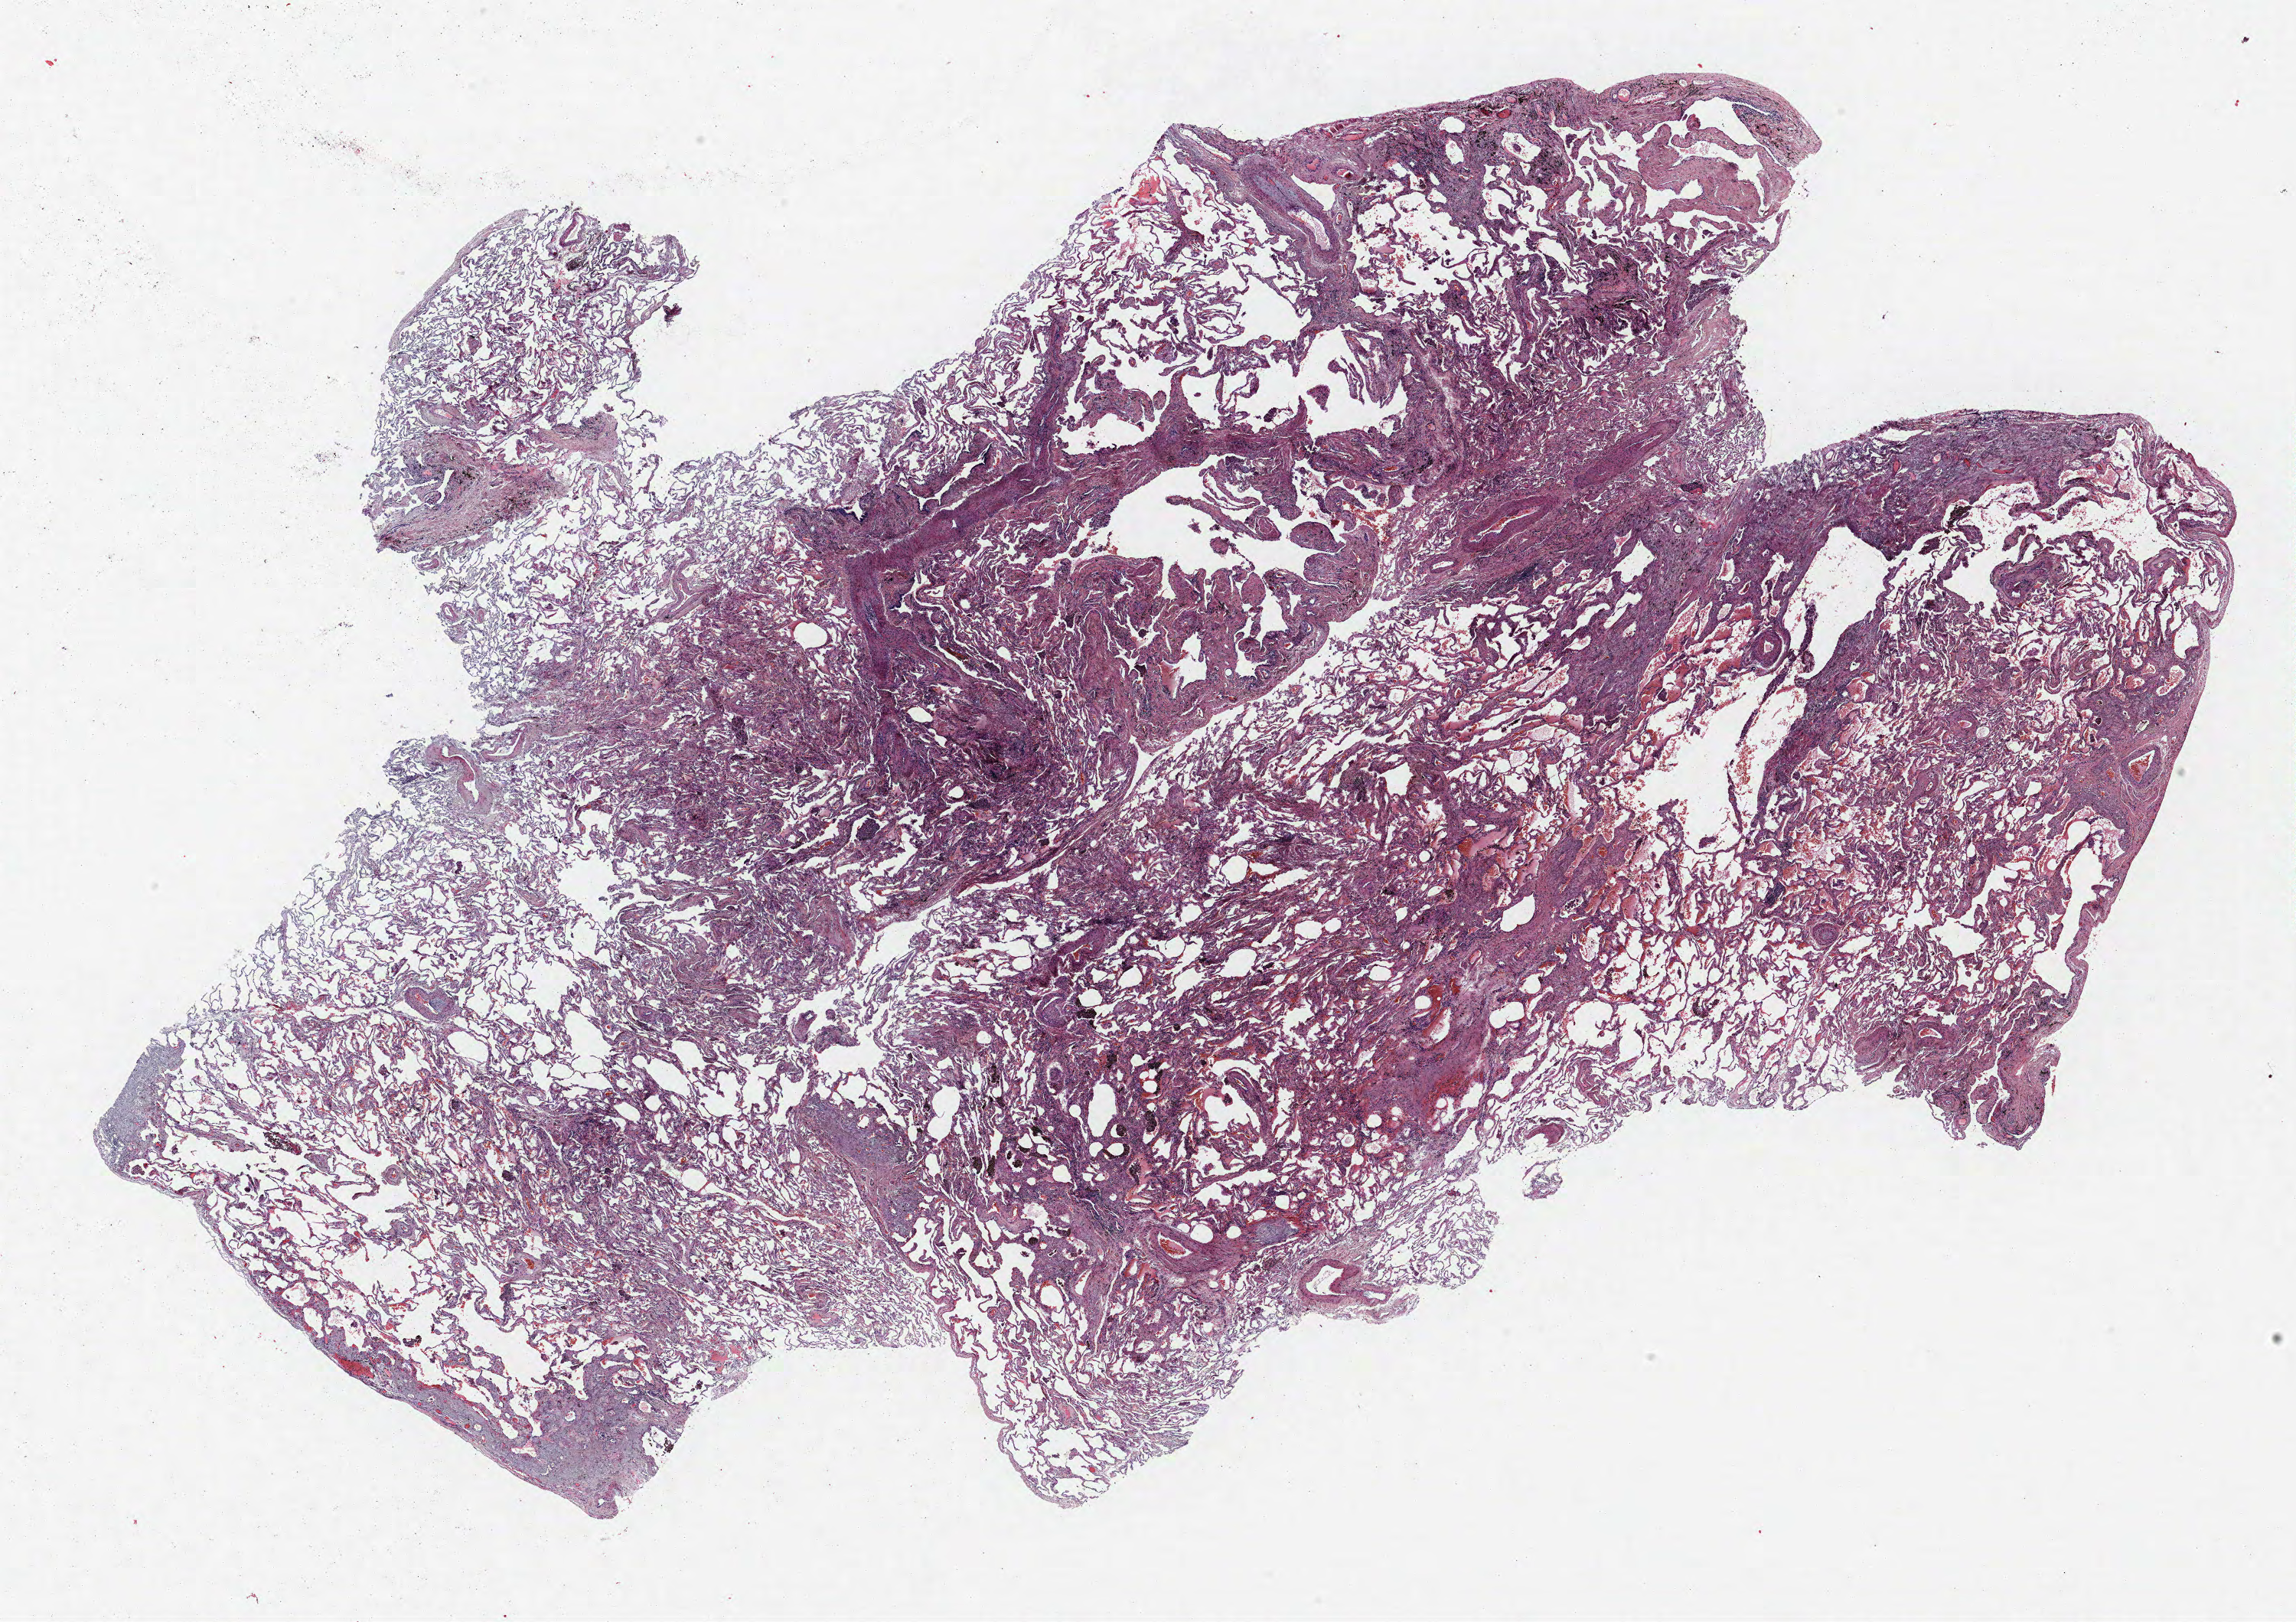
Whole-slide histology image, H&E-stained, low-resolution overview of the scanned area, about 24.0 x 17.0 mm (from a 40x scan). FFPE section. Lung tissue. Male patient, aged 64 at enrolment. Grade: poorly differentiated (G3).
• ICD-O-3 topography: upper lobe of lung (C34.1)
• participant's lung-cancer diagnosis: Squamous cell carcinoma, NOS
• primary tumour location (clinical record): left upper lobe
• stage (AJCC 6th edition): IA
• tumour size (pathology): 14 mm